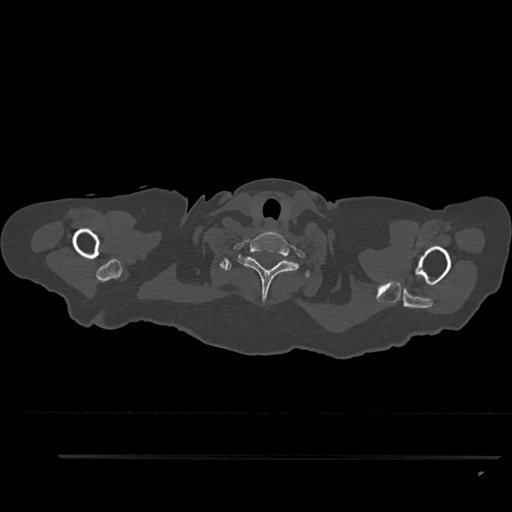
CT including the spine, one axial slice. Bone window (W 1800 / L 400 HU). 512 × 512 image matrix, field of view 408 × 408 mm. Female patient, age 44 years. Case-level facts recorded for this patient, not image findings: primary cancer: renal; vertebrae with lytic lesions (as recorded): L1.
Outlined on this slice (semi-automatically segmented with operator editing):
- T1 vertebra: bounding box <220,258,309,278> (left, top, right, bottom; pixels)